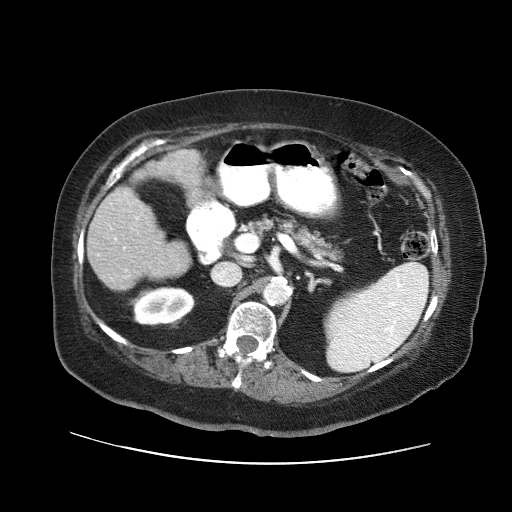
Contrast-enhanced abdominal CT (liver protocol), one axial slice. Position 19 of 71 along the scan axis. 120 kVp. Soft-tissue window (W 400 / L 40 HU). 512 × 512 image matrix, field of view 400 × 400 mm. Case-level facts recorded for this patient, not image findings: diagnosis: hepatocellular carcinoma (patient treated with transarterial chemoembolisation; whether this scan precedes or follows treatment is not stated here); TNM stage (as recorded): Stage-II; Child-Pugh class: A; tumour differentiation: poorly differentiated; tumour nodularity: multinodular.
Annotated regions visible in this slice (semi-automatically segmented with operator editing):
- liver parenchyma outside the tumour (the mass and vessels are separate outlines, so this box may not span the whole liver): bounding box [x1, y1, x2, y2] px = [88, 150, 200, 290]
- liver vessels: [114, 217, 138, 248]